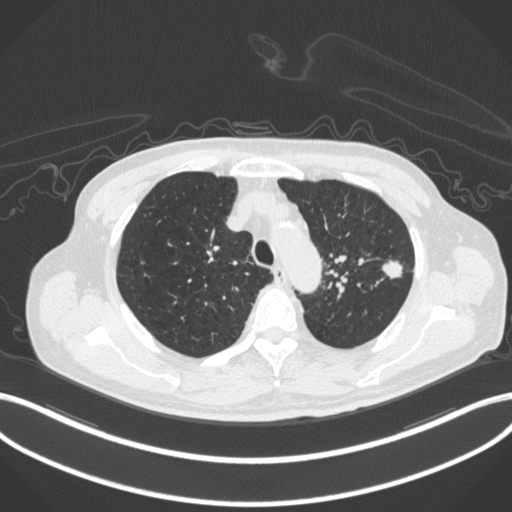
Chest CT, one axial slice. Position 345 of 420 along the scan axis. Reconstruction kernel B31f. 120 kVp. Lung window (W 1500 / L -600 HU). 1 mm slice thickness. 512 × 512 image matrix. Patient: male, 77 years. From the clinical record (not read from this slice): clinical TNM (as recorded): T3 N1 M0.
Annotated regions visible in this slice (bounding box drawn by a radiologist):
- lung tumour (recorded histology: adenocarcinoma): bounding box [x1, y1, x2, y2] px = [380, 259, 405, 281]